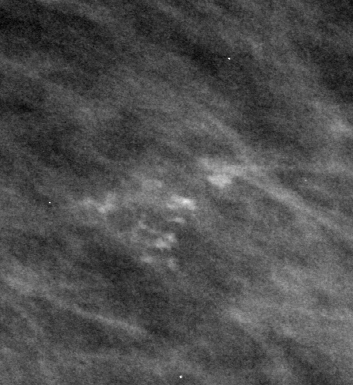
Region of interest cut from a scanned film mammogram (one marked finding); left breast; MLO view; BI-RADS breast density category 2 (scale 1–4).
- Calcifications, morphology pleomorphic, distribution clustered; BI-RADS assessment category 4; subtlety rating 4 on a 1 (subtle) to 5 (obvious) scale; pathology (as recorded): benign.